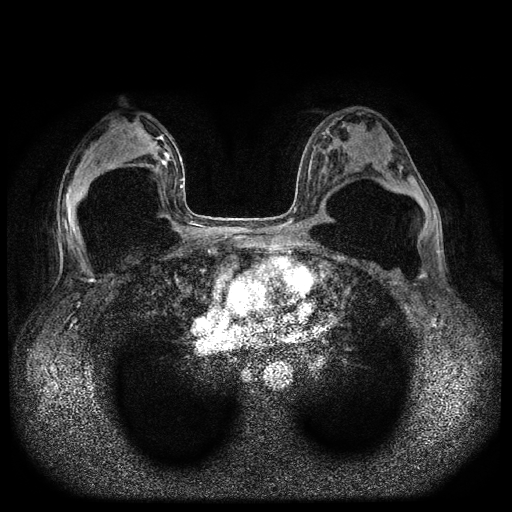
Breast MRI (dynamic contrast-enhanced, multi-phase), one axial slice; dynamic contrast-enhanced series, time point 2 of 5 at this slice position (early post-contrast); 1.5 T; TE 2.6 ms, TR 5.4 ms; 2 mm slice thickness; 512 × 512 image matrix. Patient: female, 42 years.
Outlined on this slice (semi-automatically segmented with operator editing):
- breast lesion (labelled 'tumour' in the annotation; benign lesions carry a separate 'benign' label): bounding box <161,151,170,170> (left, top, right, bottom; pixels)